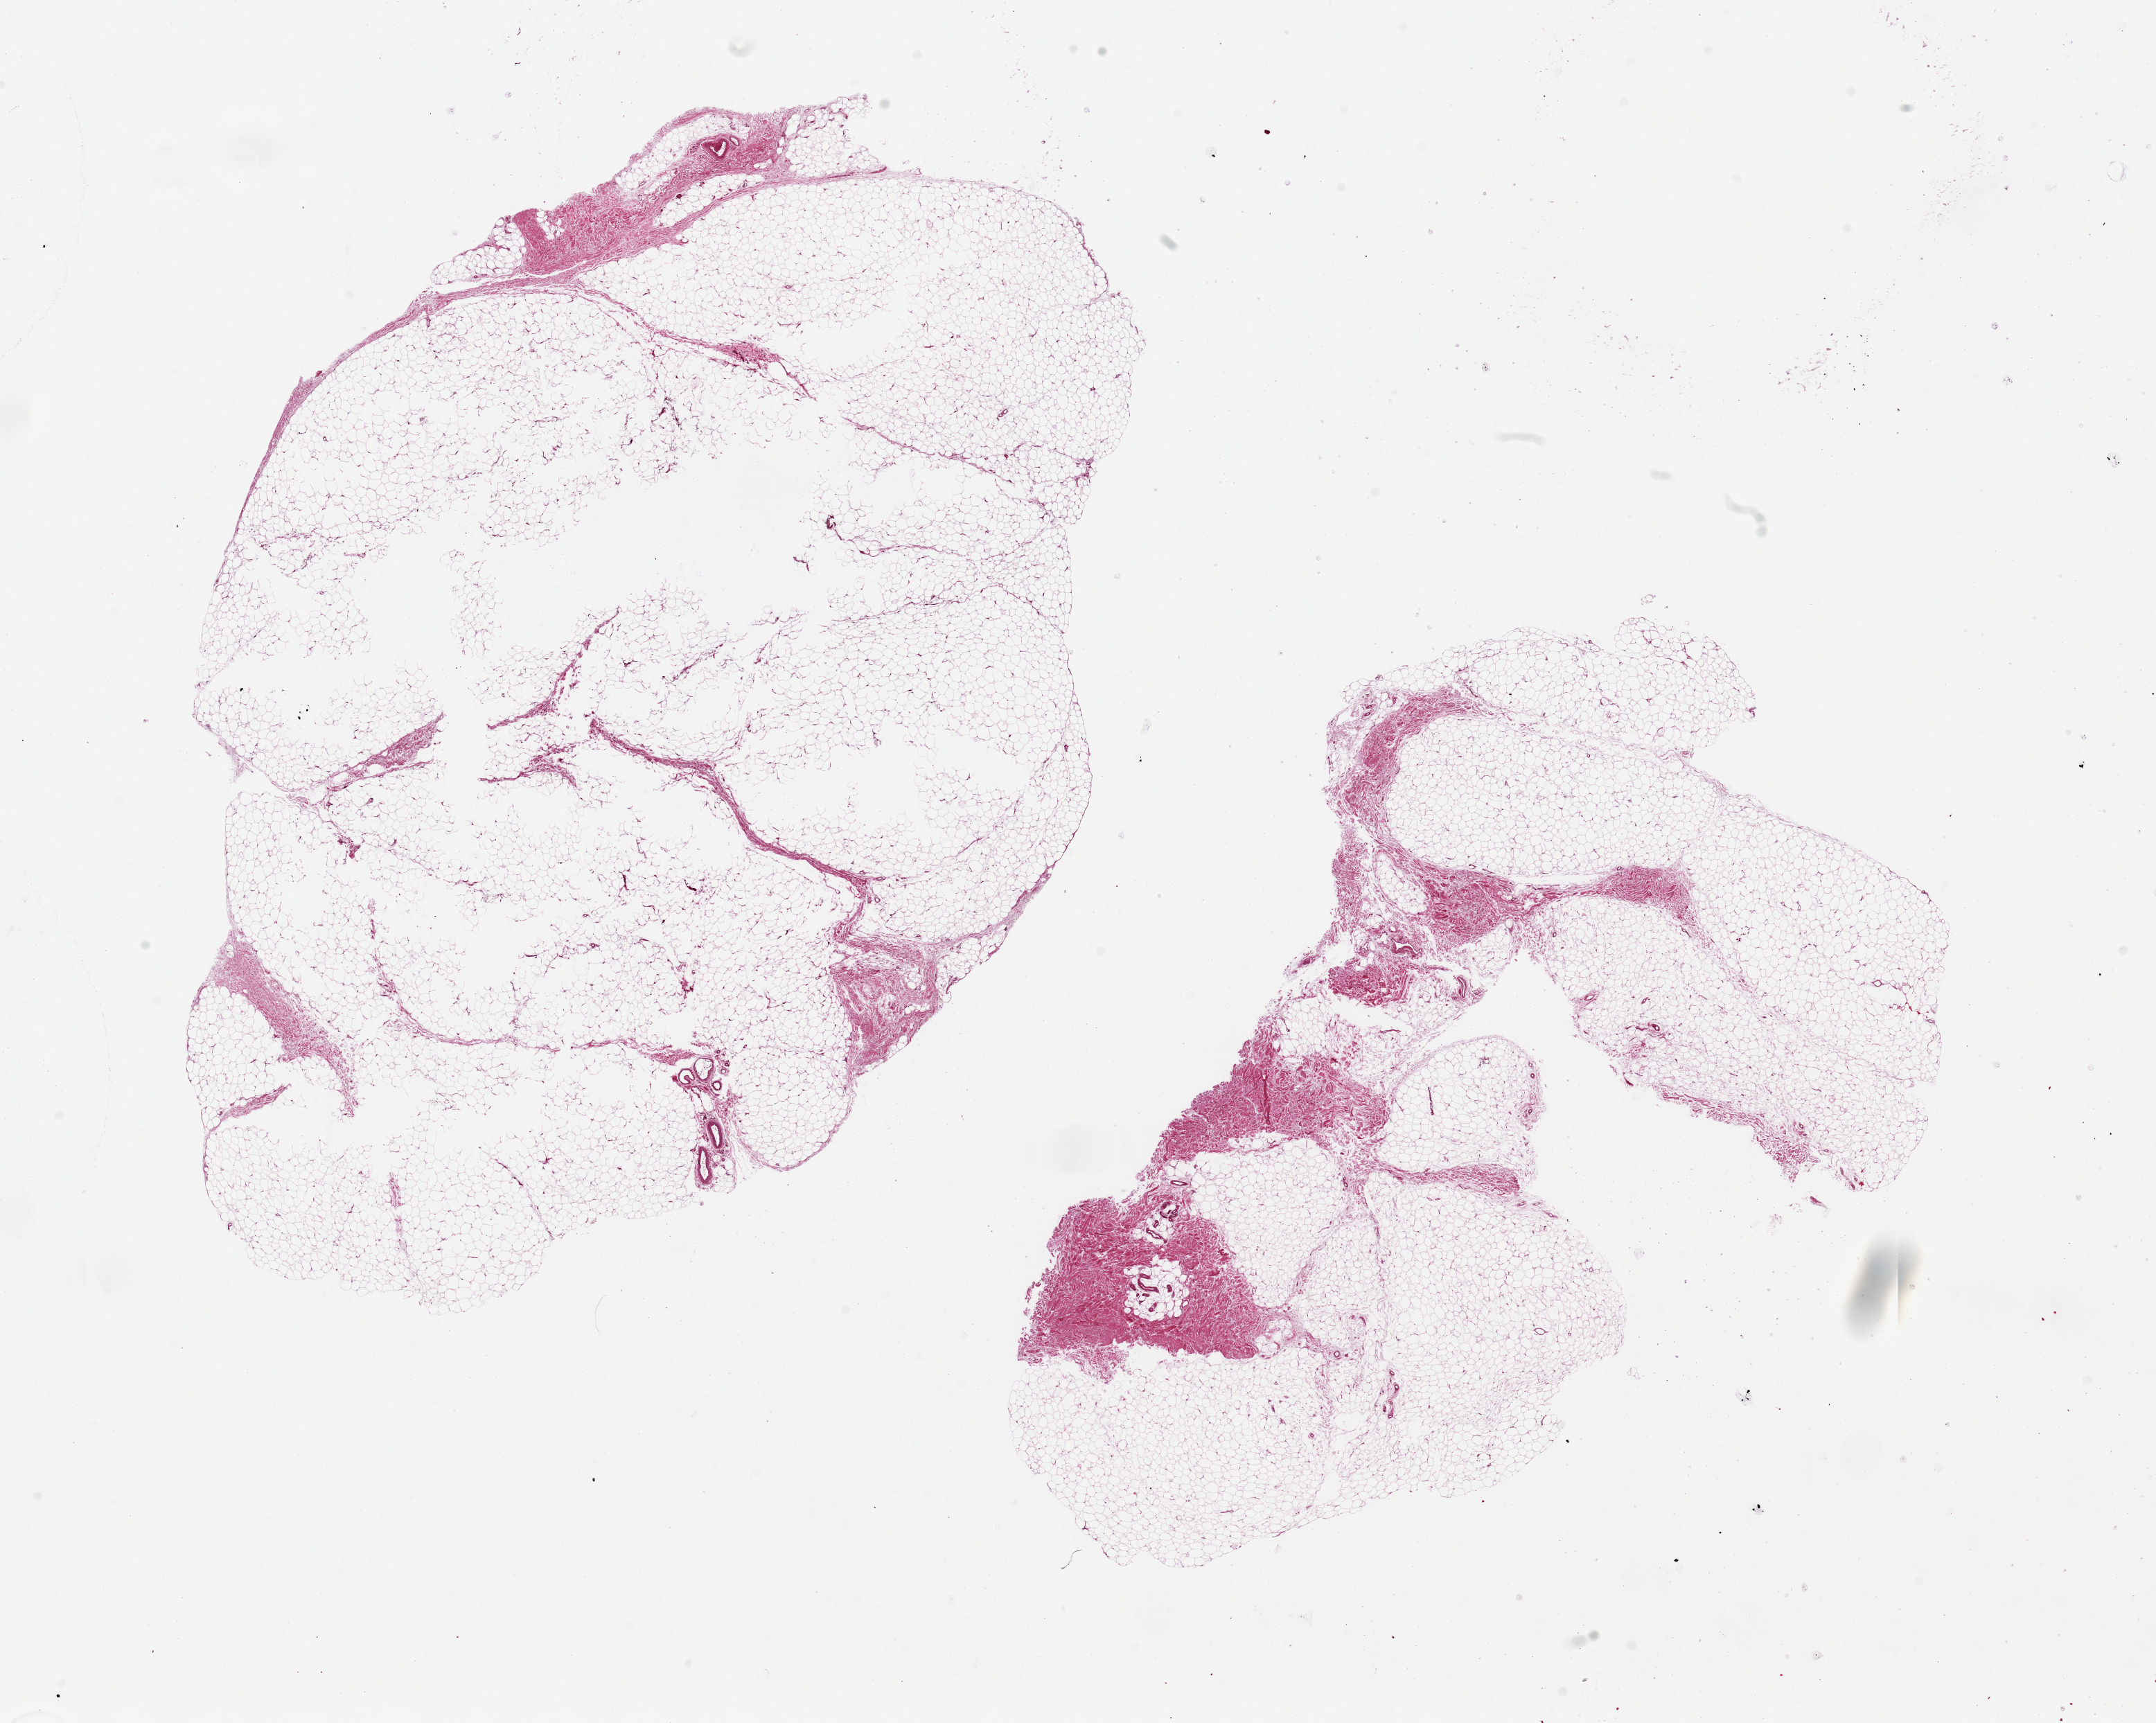
Digitized hematoxylin and eosin (H&E)-stained section — a low-resolution overview of the entire scanned area, about 24.6 x 19.7 mm (acquisition: 20x scan). PAXgene-fixed, paraffin-embedded tissue. Sampled site (target tissue): adipose tissue. Tissue donor sample. Donor: female.
Reviewer comment on this tissue sample: 2 pieces, 15x10 & 13x8mm.